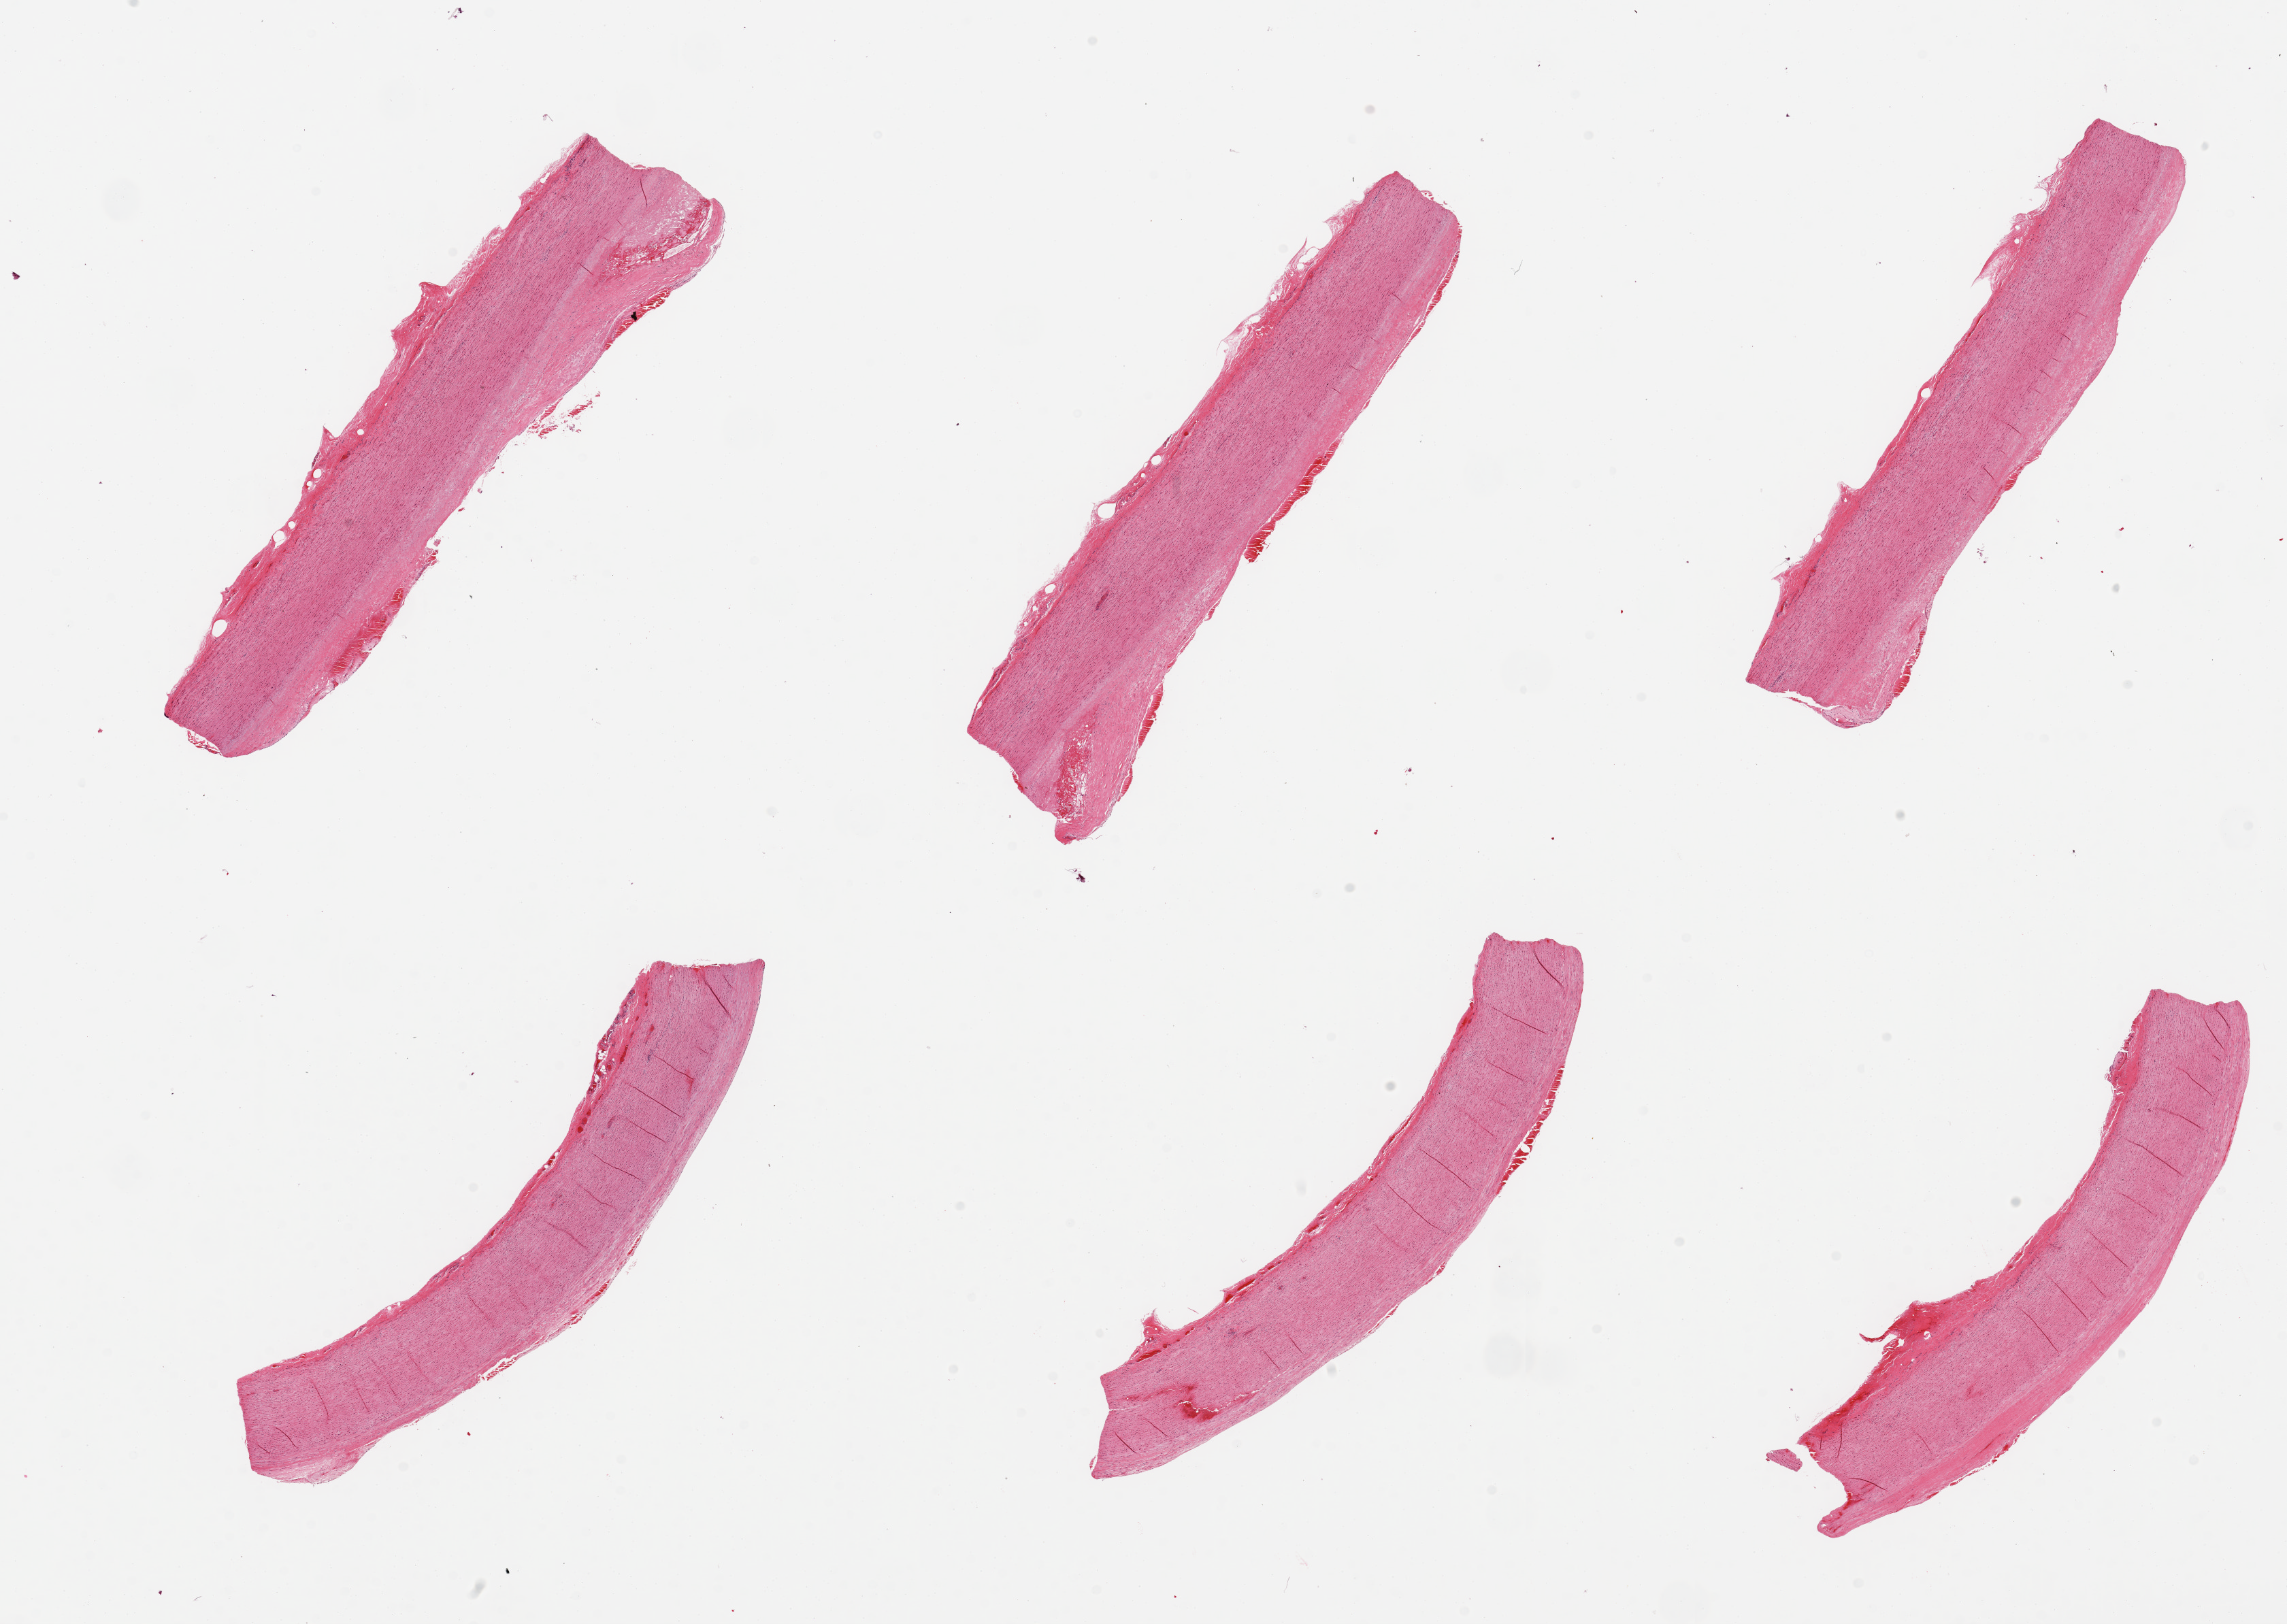
H&E whole-slide image, brightfield — whole scanned area (about 26.6 x 18.9 mm) shown as a low-resolution overview; PAXgene-fixed paraffin-embedded (PFPE) section; section of aorta (target tissue); donor tissue sample.
* pathologist's review note for this sample: 6 pieces; well dissected